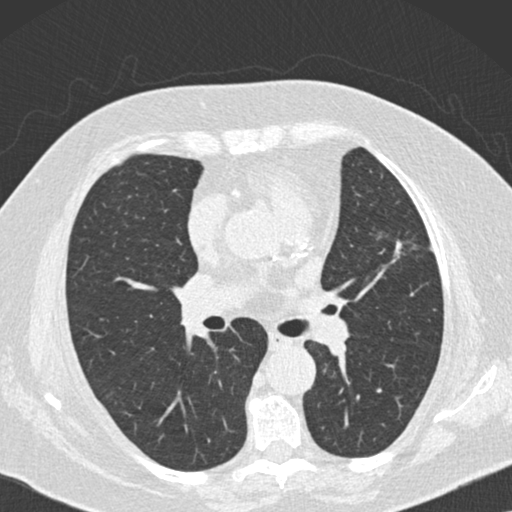
Axial slice from a low-dose chest CT screening exam. Baseline annual screen. Lung window (W 1500 / L -600 HU). 2 mm slice thickness. Slice 61 of 160 in the series. Female participant, aged 73 years at enrolment. Current smoker at enrolment.
• Lesion marked by an expert reader, bounding box <367,233,416,278> (left, top, right, bottom; pixels).
• The exam's reader record, not a measurement of the box and not confirmed to be the same lesion: non-calcified nodule or mass ≥4 mm, right lower lobe, 7 × 7 mm, soft tissue attenuation.
• Note: the box lies in the patient's left hemithorax on this image, whereas the reader's record names the right lung; they may be different findings.
• Official screen result: positive, change unspecified: nodule(s) >= 4 mm or enlarging nodule(s), mass(es), or other non-specific abnormalities suspicious for lung cancer.
• Participant outcome: lung cancer diagnosed 504 days after this screen (after the second annual screen) — adenocarcinoma, NOS, left upper lobe, moderately differentiated (G2), stage IIIB (AJCC 6th edition), 12 mm at pathology.